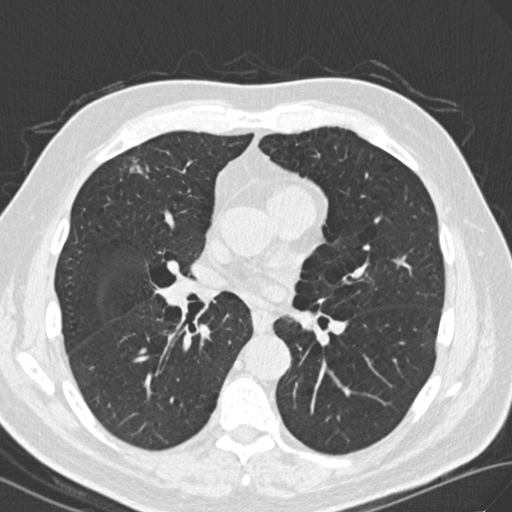
Chest CT (low-dose screening protocol), one axial image; second annual screen; lung window (W 1500 / L -600 HU); standard (soft-tissue) reconstruction kernel (B30f); 120 kVp. Male, age 69 years at enrolment. Current smoker at enrolment.
Expert-annotated lung lesion, box from (x=107, y=140) to (x=163, y=196) px. The screening reader recorded 3 non-calcified nodules or masses ≥4 mm on this exam (right upper lobe, right lower lobe, right lower lobe); which of them this box marks is not recorded. Official screen result: positive, other.